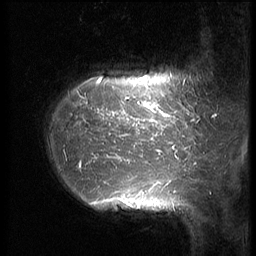
Breast MRI (dynamic contrast-enhanced), one sagittal slice; position 12 of 64 along the scan axis; 3 images stored at this slice position (order not interpretable as contrast timing); 1.5 T; TE 4.2 ms, TR 9 ms; 2.5 mm slice thickness; 256 × 256 image matrix, field of view 180 × 180 mm. Patient: female, 39 years. Case-level facts recorded for this patient, not image findings: setting: breast cancer imaged before/during neoadjuvant chemotherapy; receptor status: HER2-positive.
Outlined on this slice (semi-automatically segmented with operator editing):
- analysis volume of interest (the breast-tissue region the enhancement analysis was run in; not a lesion): bounding box <43,47,210,239> (left, top, right, bottom; pixels)
- tumour enhancement mask (voxels above the 140 % enhancement threshold inside the analysis volume of interest): <76,76,198,185>